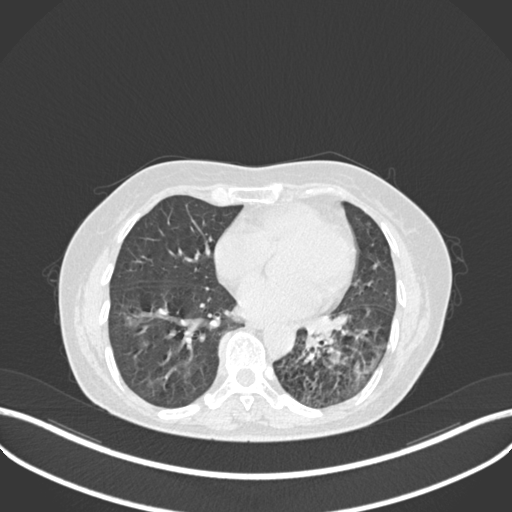
Chest CT, one axial slice. Slice 106 of 270 in the series (ordered by position). Reconstruction kernel B30f. 120 kVp. Lung window (W 1500 / L -600 HU). 1 mm slice thickness. 512 × 512 image matrix, field of view 400 × 400 mm. Female patient, age 63 years. Case-level facts recorded for this patient, not image findings: clinical TNM (as recorded): T1b N0 M0.
Structures marked on this image (rectangle marked by the reading radiologist):
- lung tumour (recorded histology: adenocarcinoma): box from (x=301, y=314) to (x=348, y=349) px